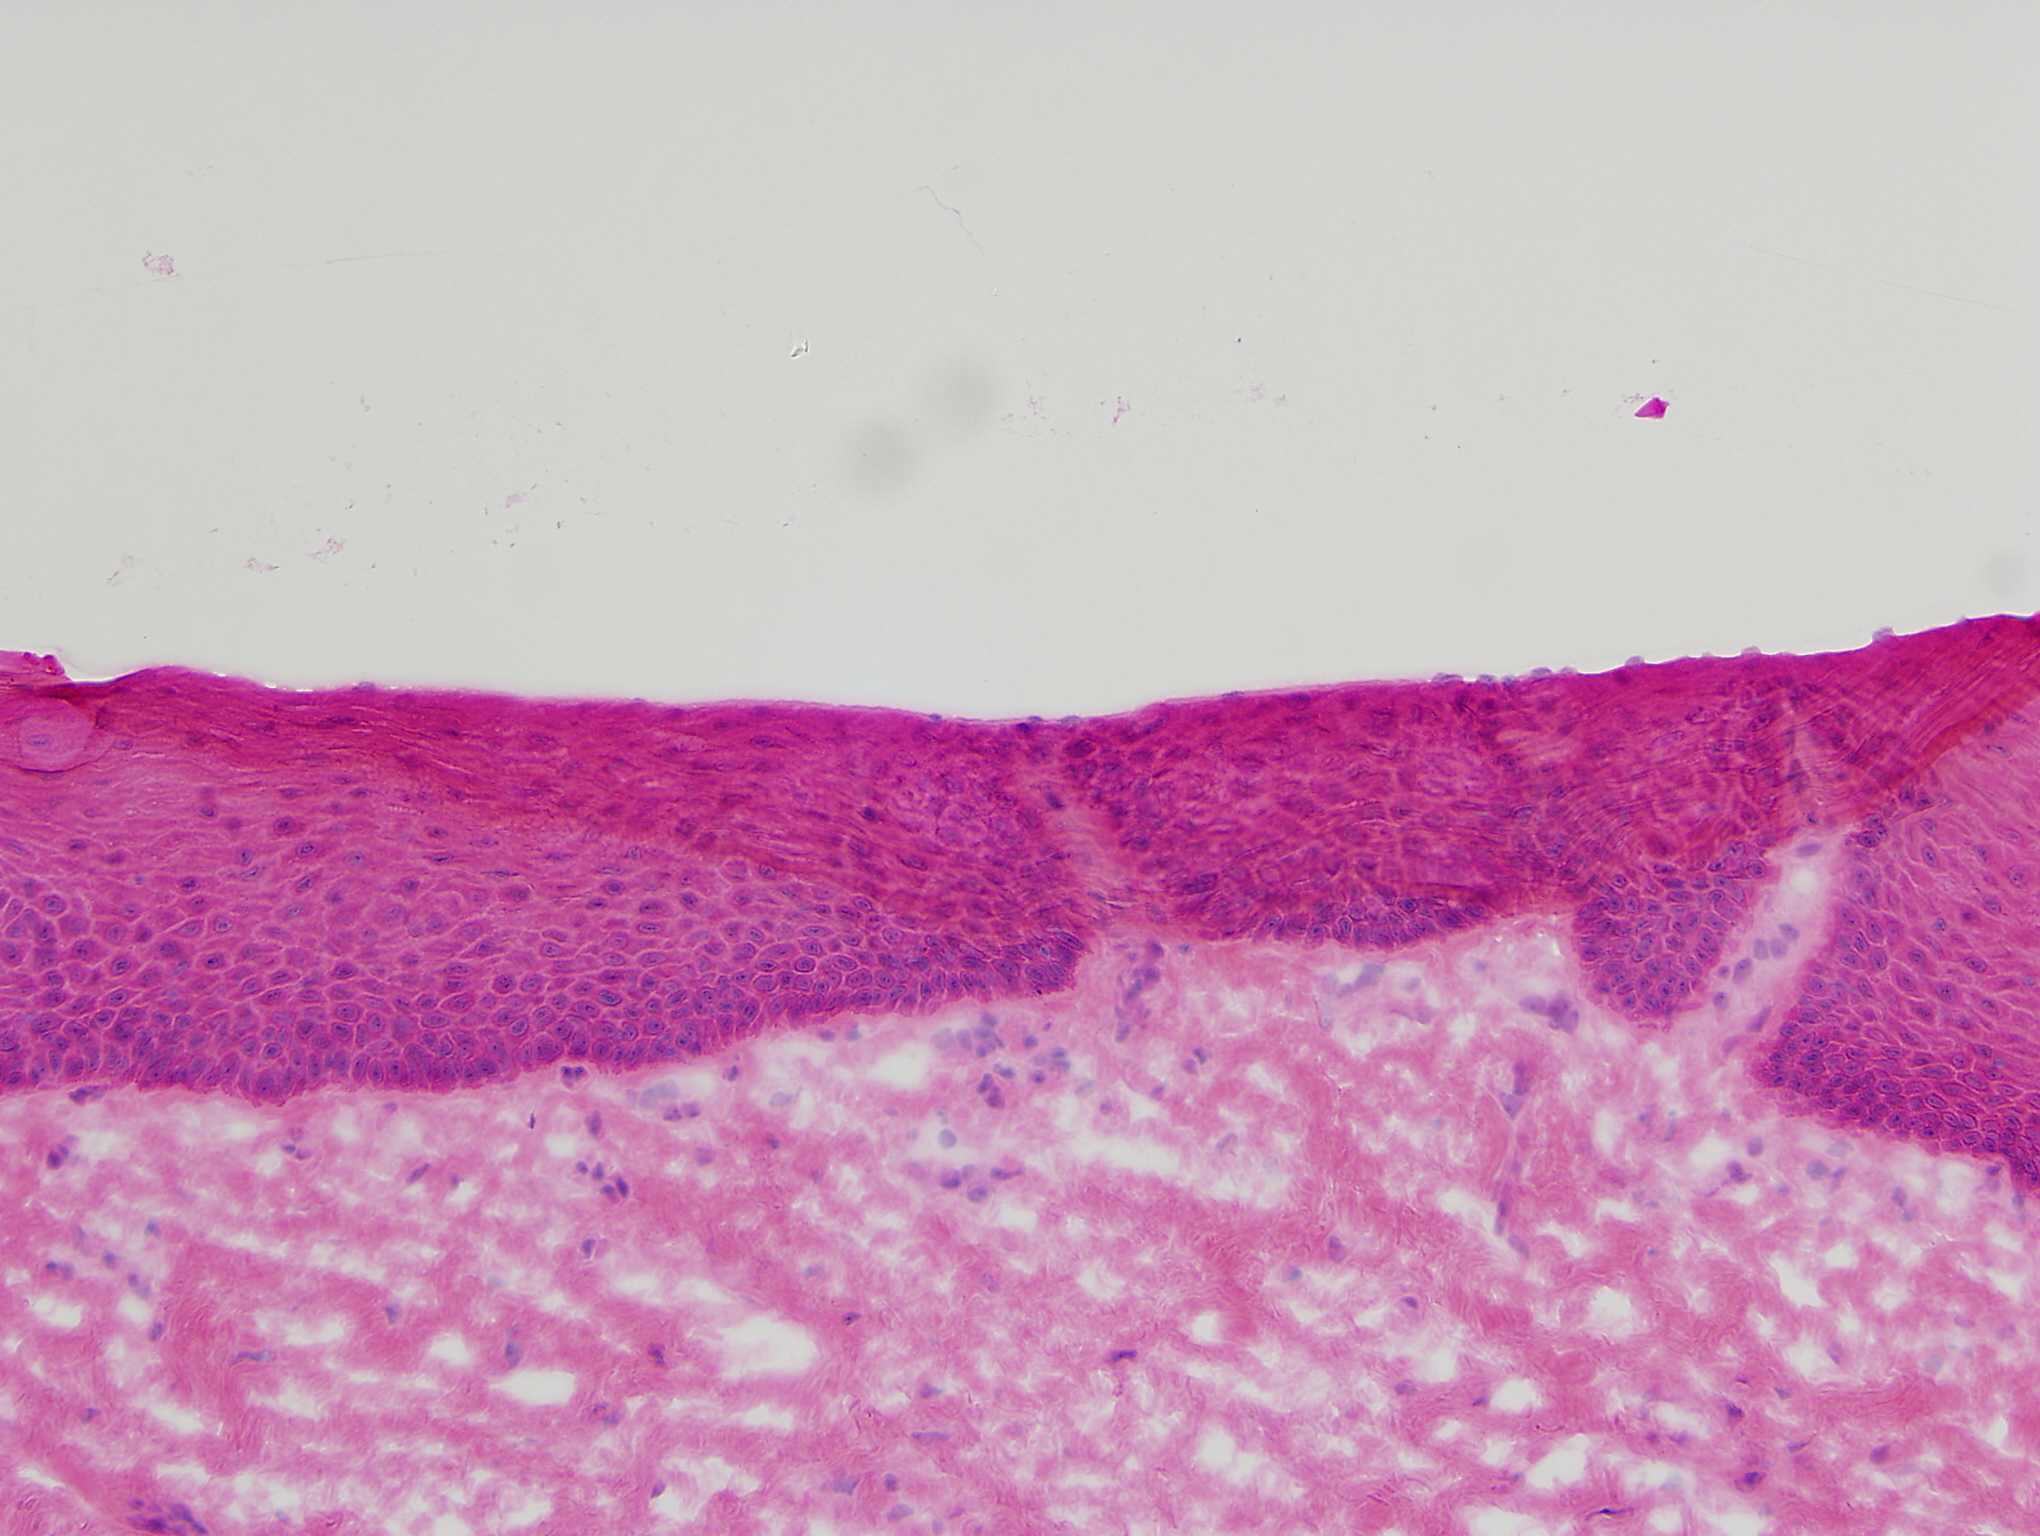
H&E-stained image of one small field of the section — about 1.0 x 0.8 mm across, frozen section from the top of the tissue portion, solid tissue normal (non-tumour tissue) sample from the head and neck. Patient: female, age at initial diagnosis 87 years.
* this section: solid tissue normal (non-tumour) sample from the same patient
* patient diagnosis: Squamous cell carcinoma, NOS (tongue, NOS)